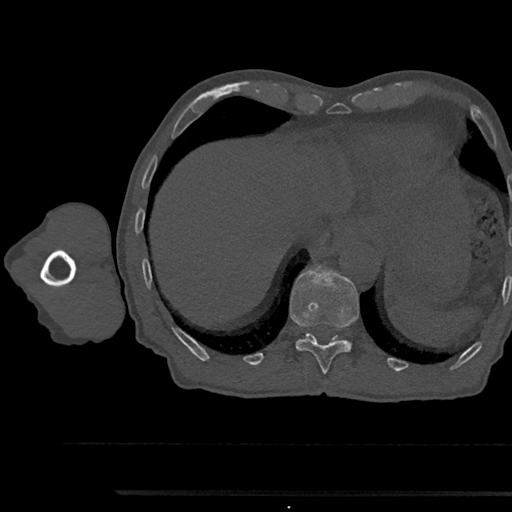
CT including the spine, one axial slice. Slice 775 of 797 in the series (ordered by position). Reconstruction kernel Br40s/3. 120 kVp. Bone window (W 1800 / L 400 HU). 512 × 512 image matrix, field of view 367 × 367 mm. Male patient, age 79 years. Case-level facts recorded for this patient, not image findings: primary cancer: prostate.
Structures marked on this image (semi-automatic segmentation, software-assisted and operator-edited):
- T11 vertebra: bounding box [x1, y1, x2, y2] px = [290, 266, 359, 374]